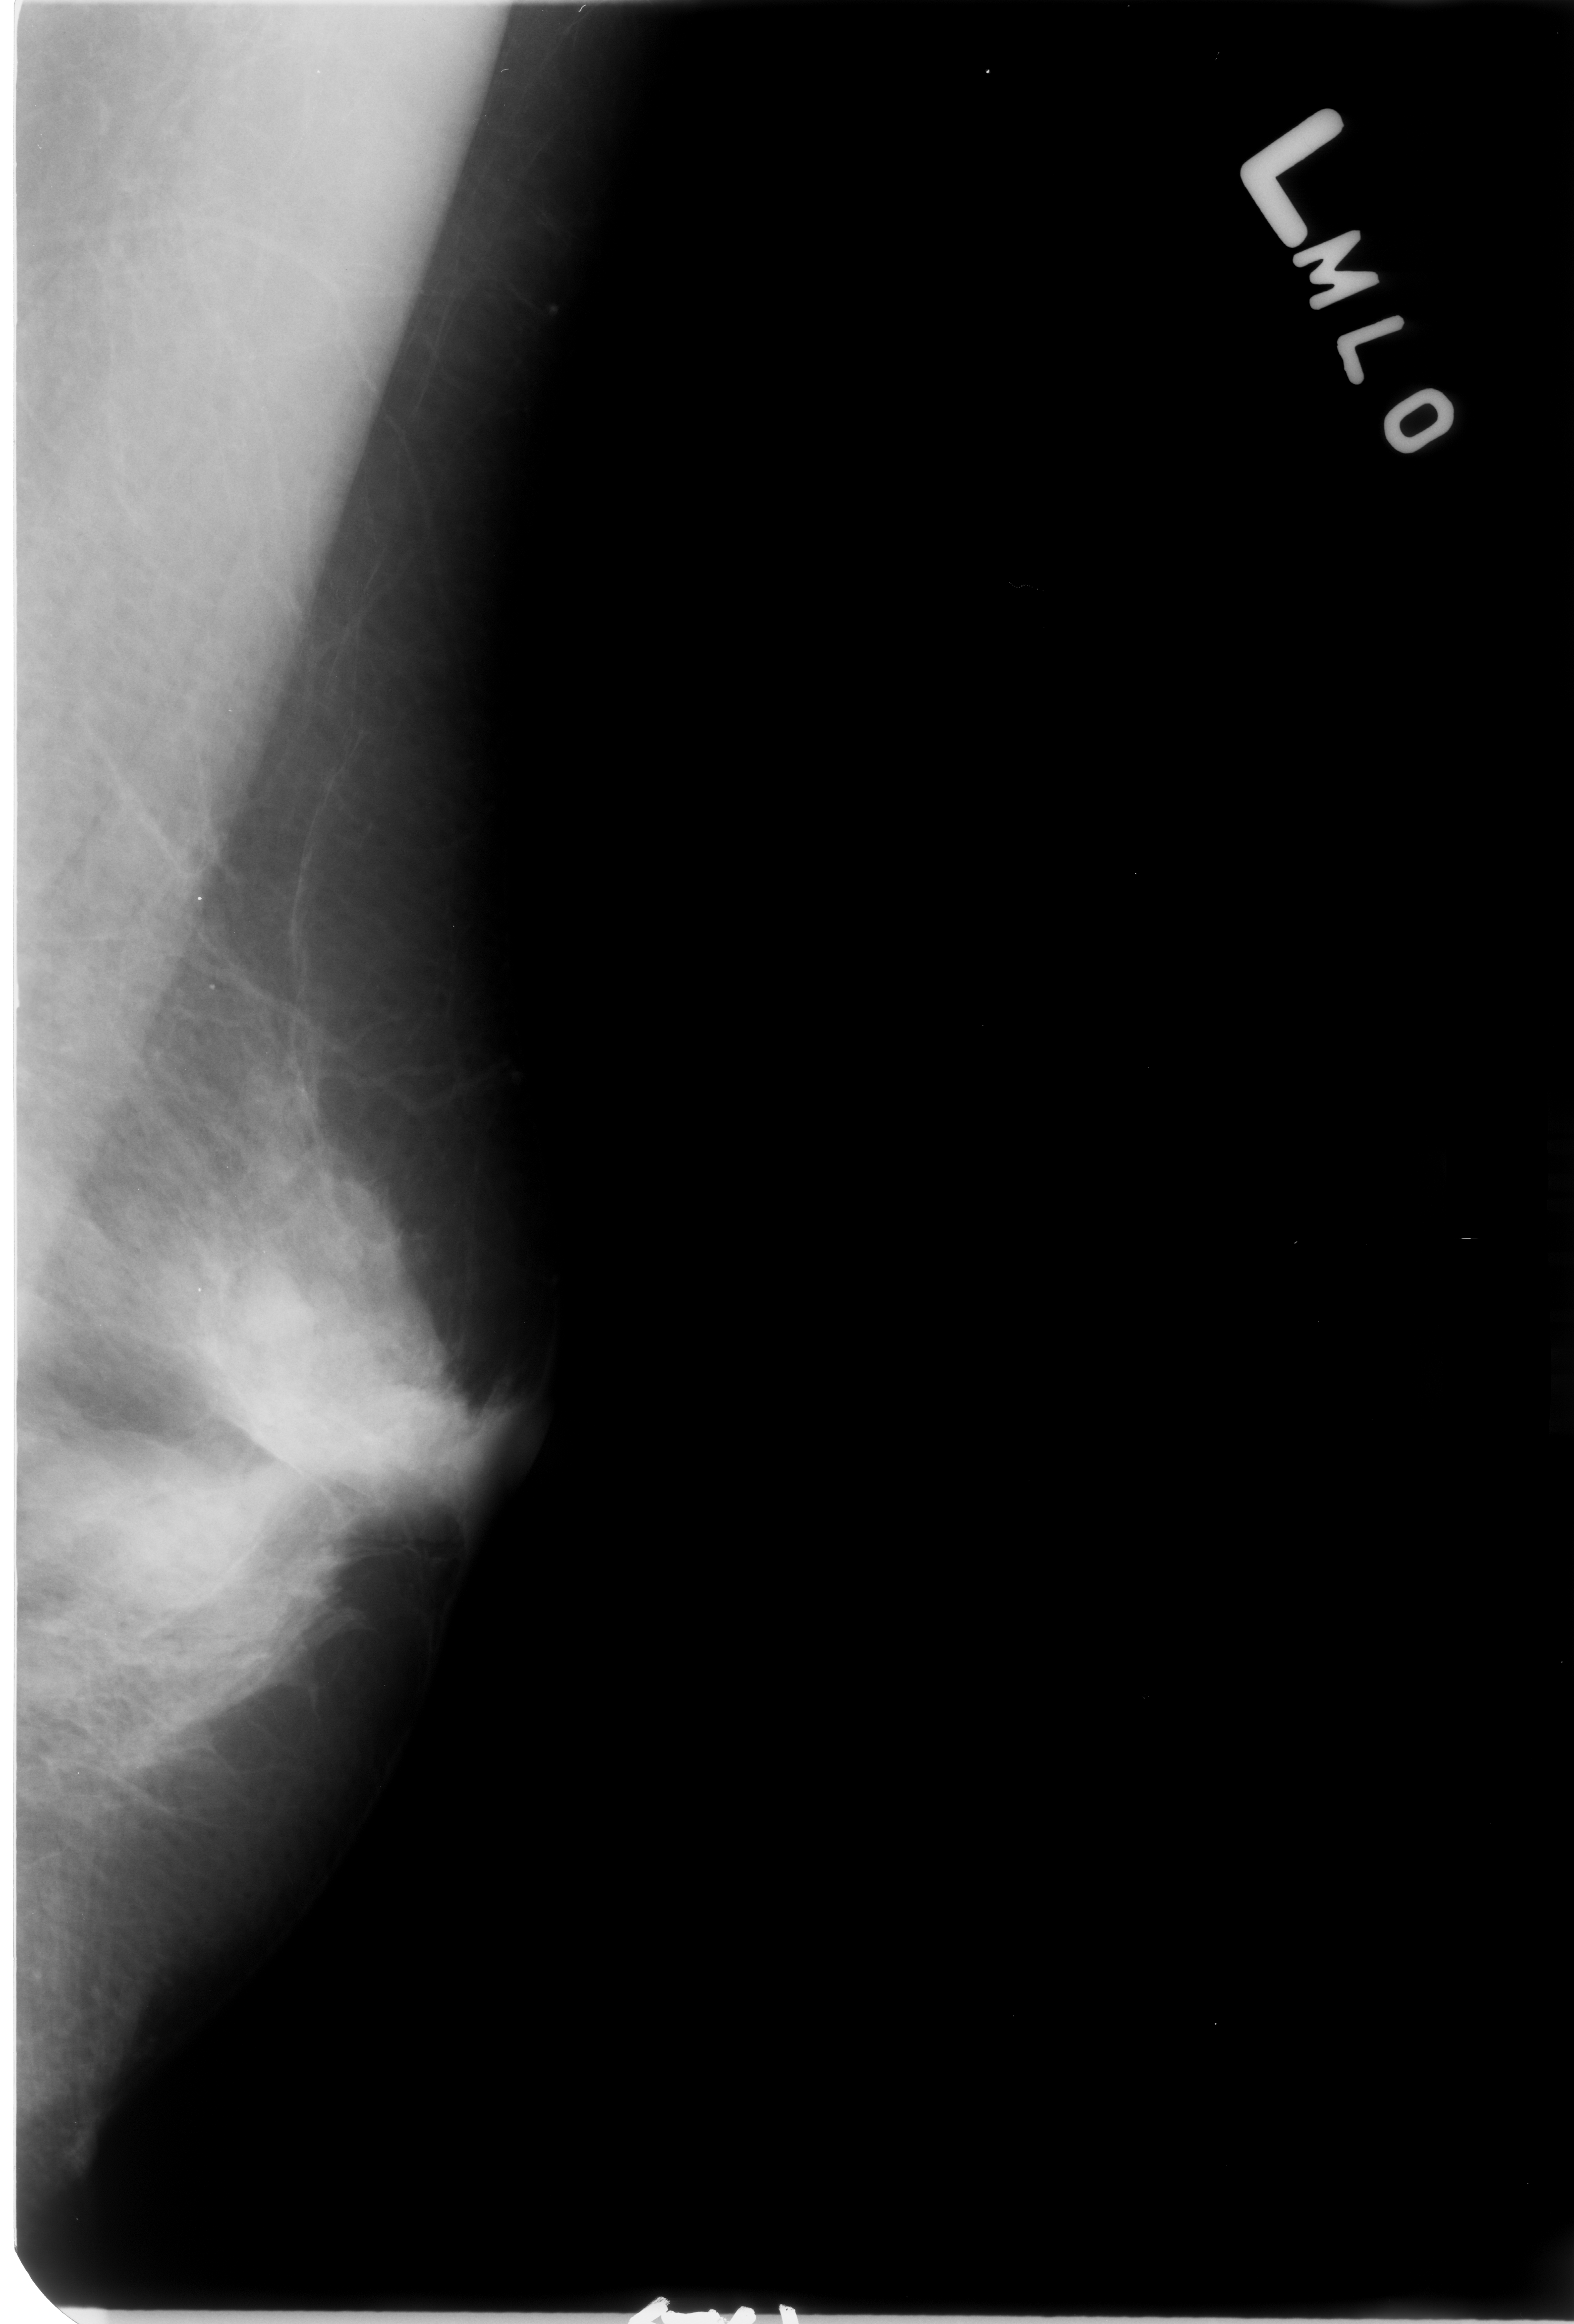
Scanned film-screen mammogram, left breast, MLO view, breast composition: heterogeneously dense (BI-RADS density category 3 of 4).
Abnormality record for this image: mass, shape architectural distortion, margins ill defined; BI-RADS assessment category 3; benign; no additional work-up was recommended (benign without callback).